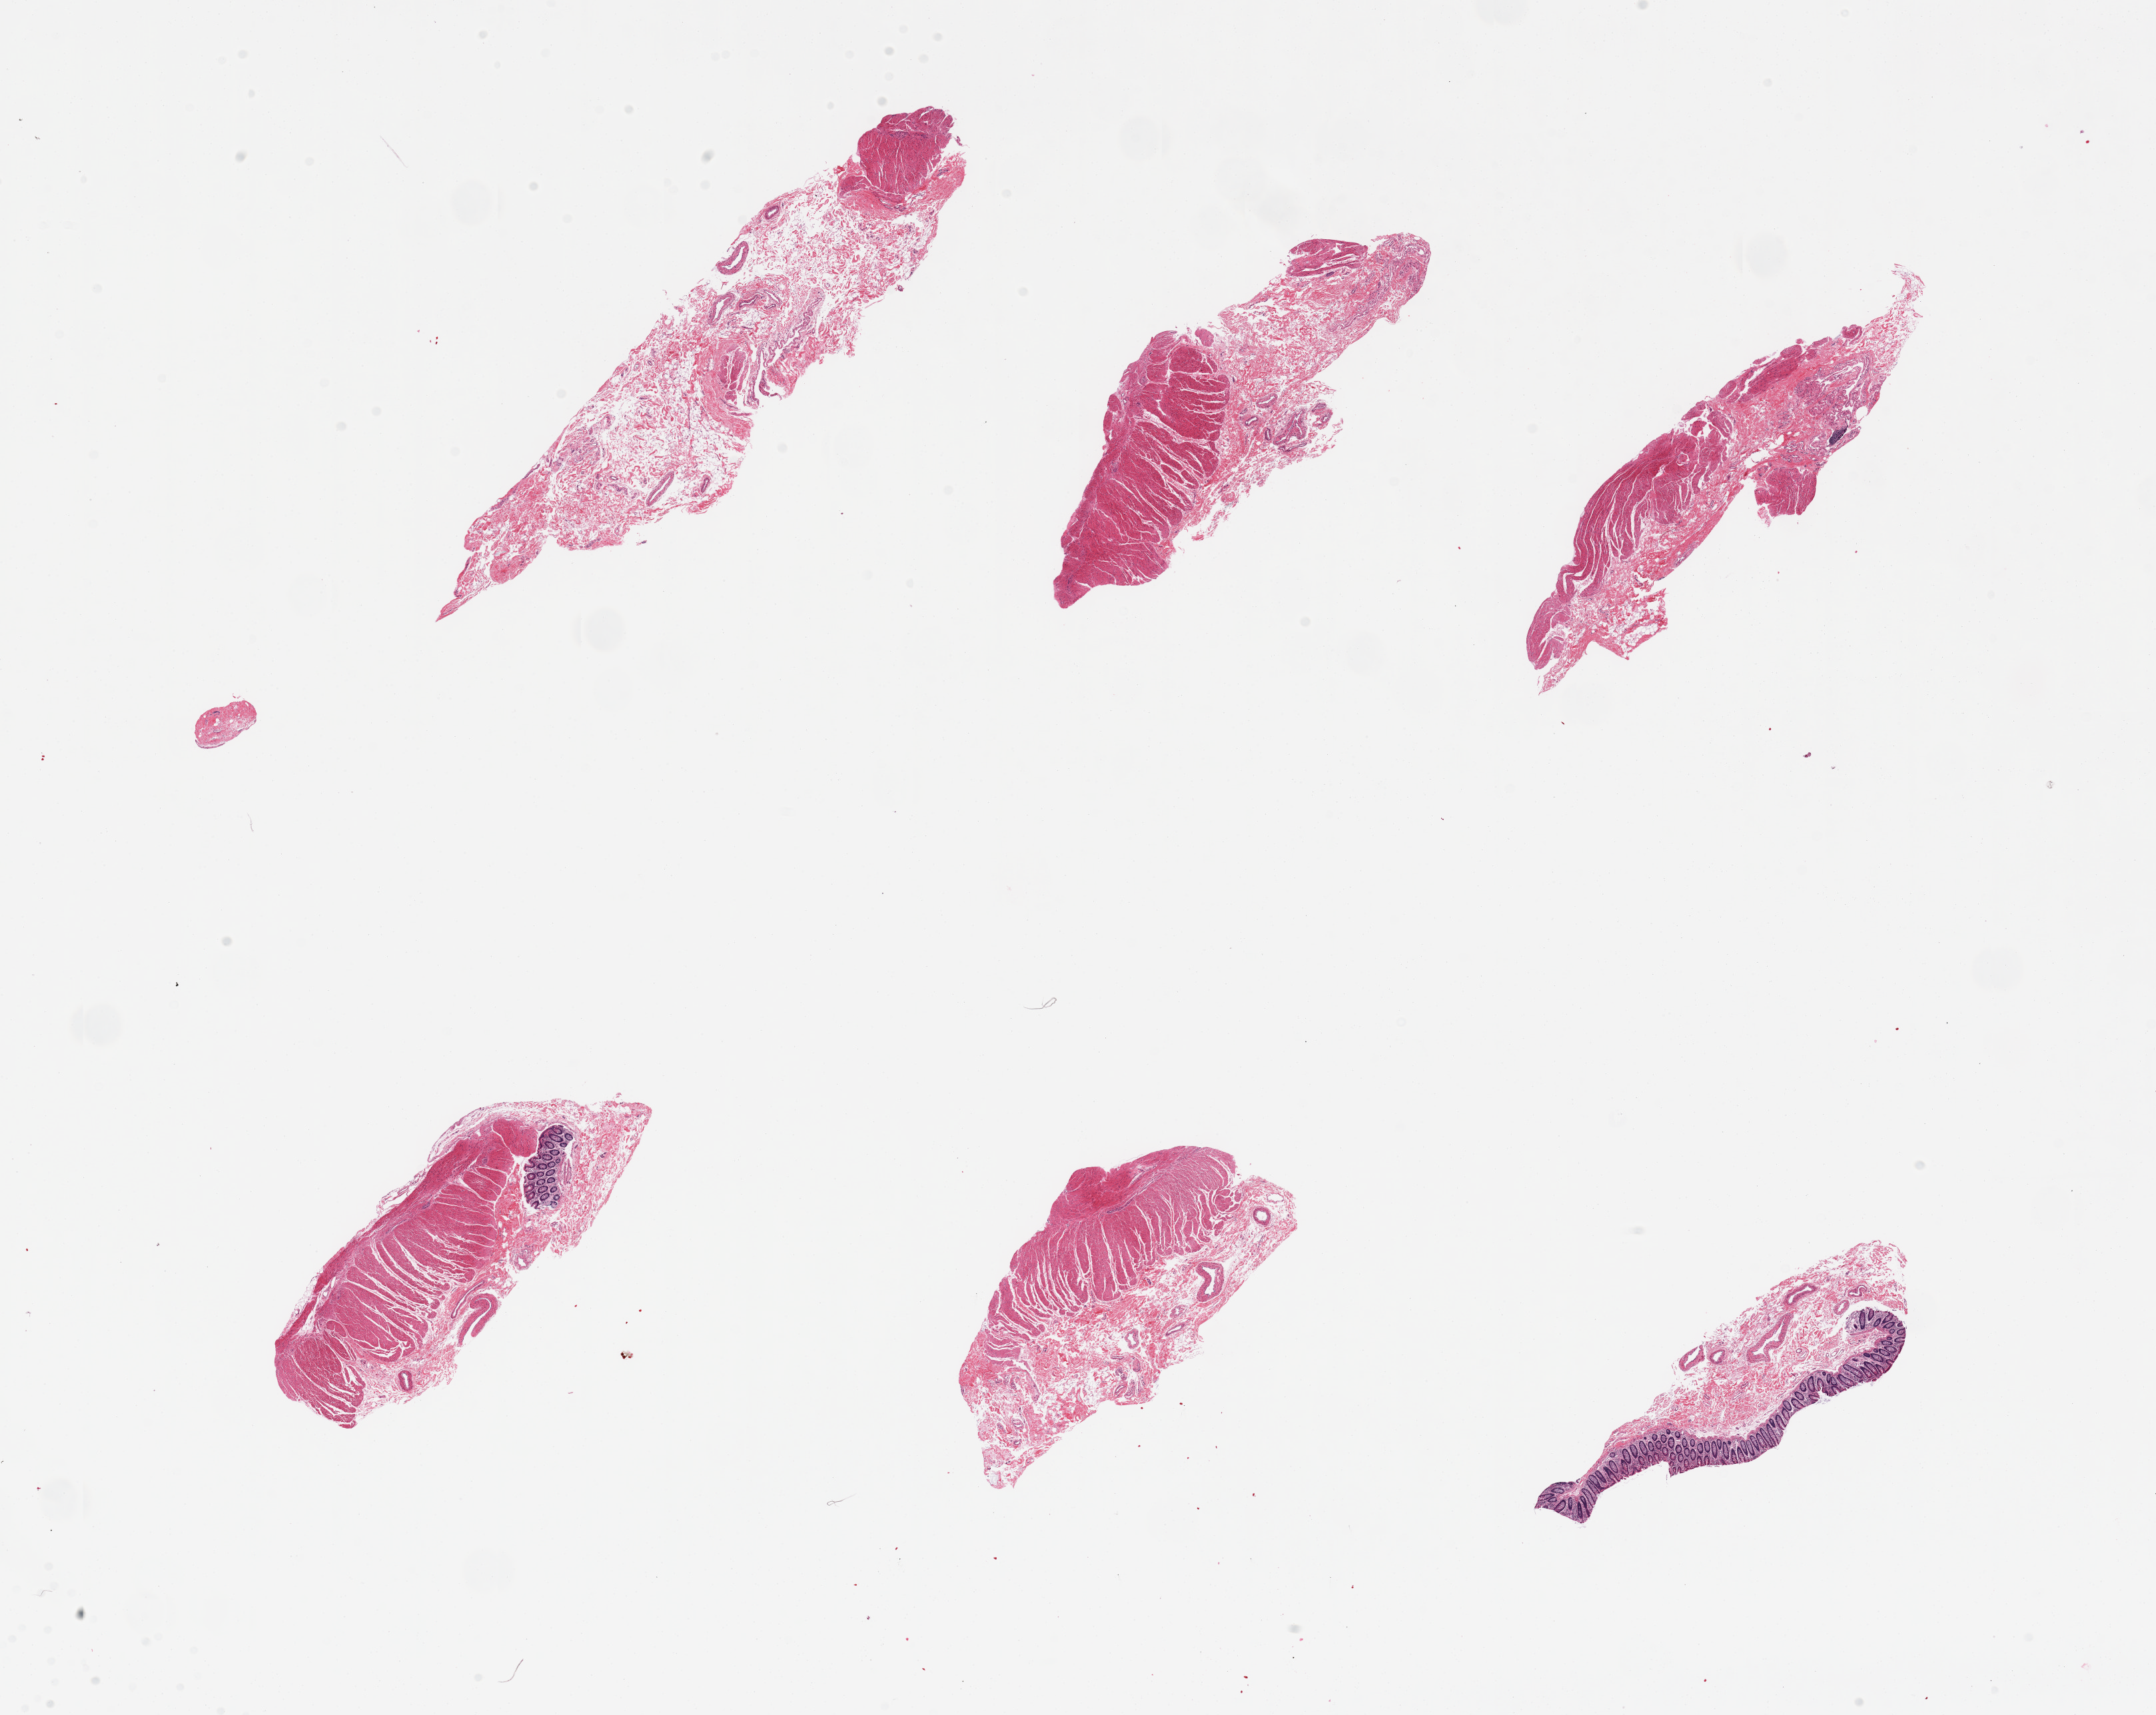
Whole-slide image, haematoxylin and eosin stain — shown as a low-resolution overview of the whole scanned area (about 25.6 x 20.4 mm, from a 20x scan); PAXgene-fixed paraffin-embedded (PFPE) section; section of transverse colon (target tissue); tissue donor sample. Donor sex: female.
Review note (as recorded): 6 pieces; poorly sampled: mucosa in 2 pieces, muscle in 5.